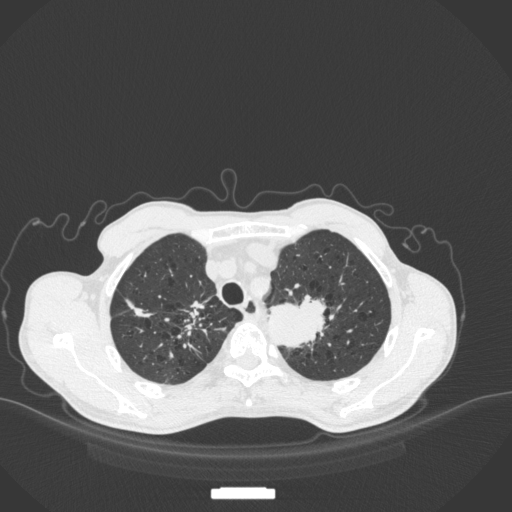
Chest CT, one axial slice. Position 349 of 394 along the scan axis. Lung window (W 1500 / L -600 HU). 512 × 512 image matrix, field of view 400 × 400 mm. Patient: male, 65 years. From the clinical record (not read from this slice): clinical TNM (as recorded): T2b N0 M0; histopathological grade: G2.
Structures marked on this image (rectangle marked by the reading radiologist):
- lung tumour (recorded histology: adenocarcinoma): box from (x=263, y=291) to (x=333, y=353) px